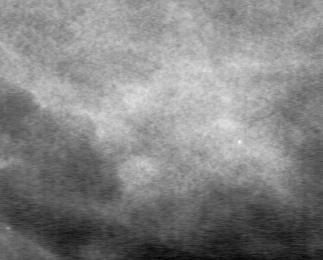
Region of interest cut from a scanned film mammogram (one marked finding), right breast, MLO view, BI-RADS breast density category 2 (scale 1–4).
Finding: mass, shape irregular, margins ill defined; BI-RADS assessment category 4; subtlety rating 1 on a 1 (subtle) to 5 (obvious) scale; pathology (as recorded): benign.